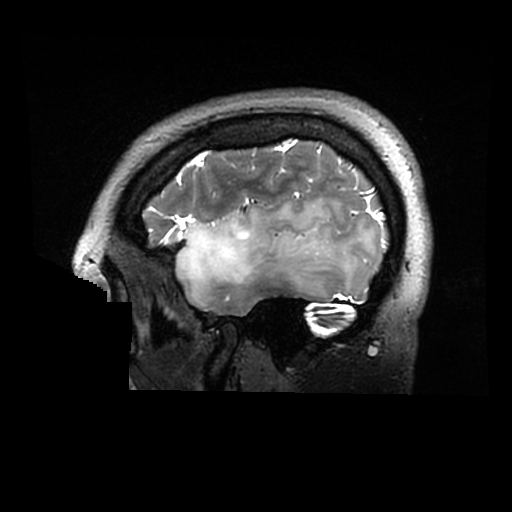
Brain MRI from a brain-tumour surgery series, one sagittal slice; position 238 of 320 along the scan axis; 0.6 mm slice thickness; 512 × 512 image matrix. Case-level facts recorded for this patient, not image findings: histopathology: Astrocytoma; WHO grade: 2; IDH mutation: yes.
Annotated regions visible in this slice (expert manual segmentation):
- tumour: box from (x=176, y=198) to (x=367, y=299) px